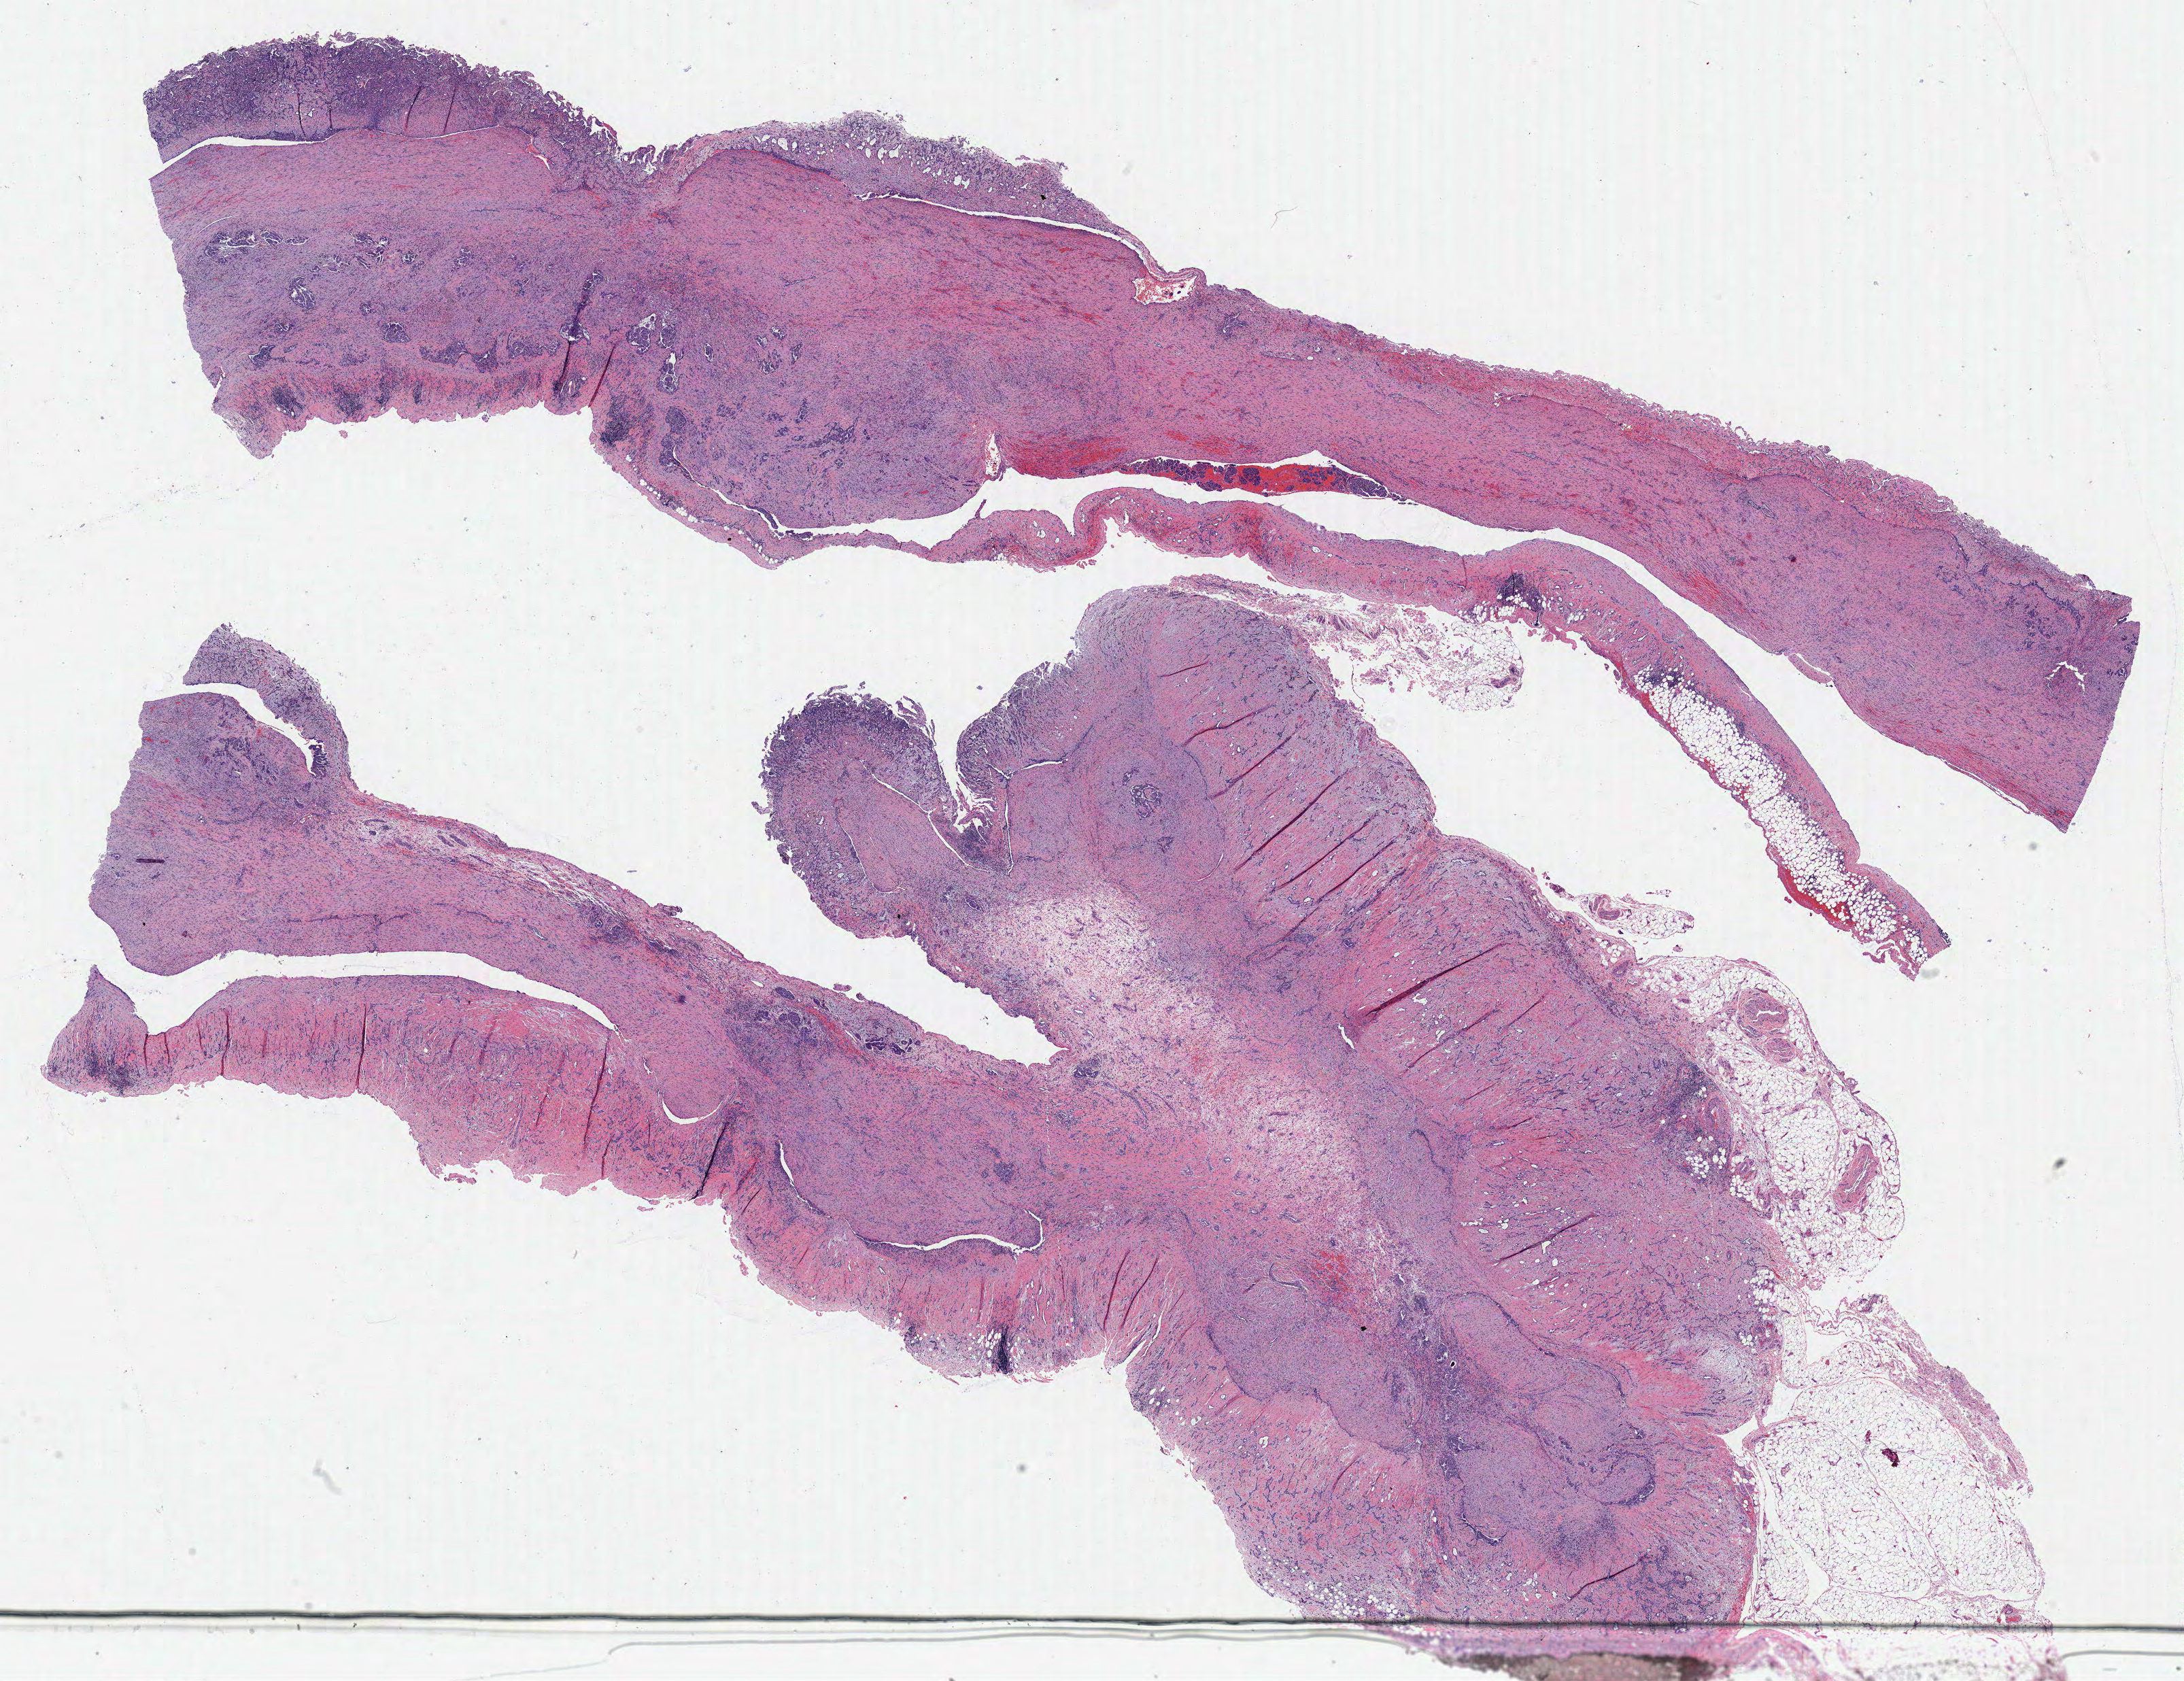
Whole-slide histology image, Hematoxylin and eosin (H&E) stained, a low-resolution overview of the entire scanned area, about 25.6 x 19.7 mm; FFPE section; sample: primary tumour, mesothelium. Patient: male, age at initial diagnosis 71 years.
• AJCC pathologic stage: IV (7th edition)
• TNM: T4 N0 M0
• pathologic diagnosis: Mesothelioma, biphasic, malignant (pleura, NOS)
• laterality: right